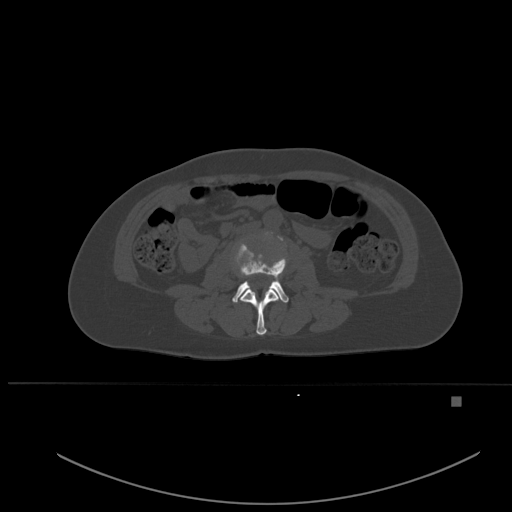
CT including the spine, one axial slice. Slice 202 of 651 in the series (ordered by position). Bone window (W 1800 / L 400 HU). 512 × 512 image matrix, field of view 443 × 443 mm. Female patient, age 49 years. Case-level facts recorded for this patient, not image findings: primary cancer: breast.
Structures marked on this image (semi-automatically segmented with operator editing):
- L2 vertebra: bounding box <240,263,279,335> (left, top, right, bottom; pixels)
- L3 vertebra: <232,237,289,303>